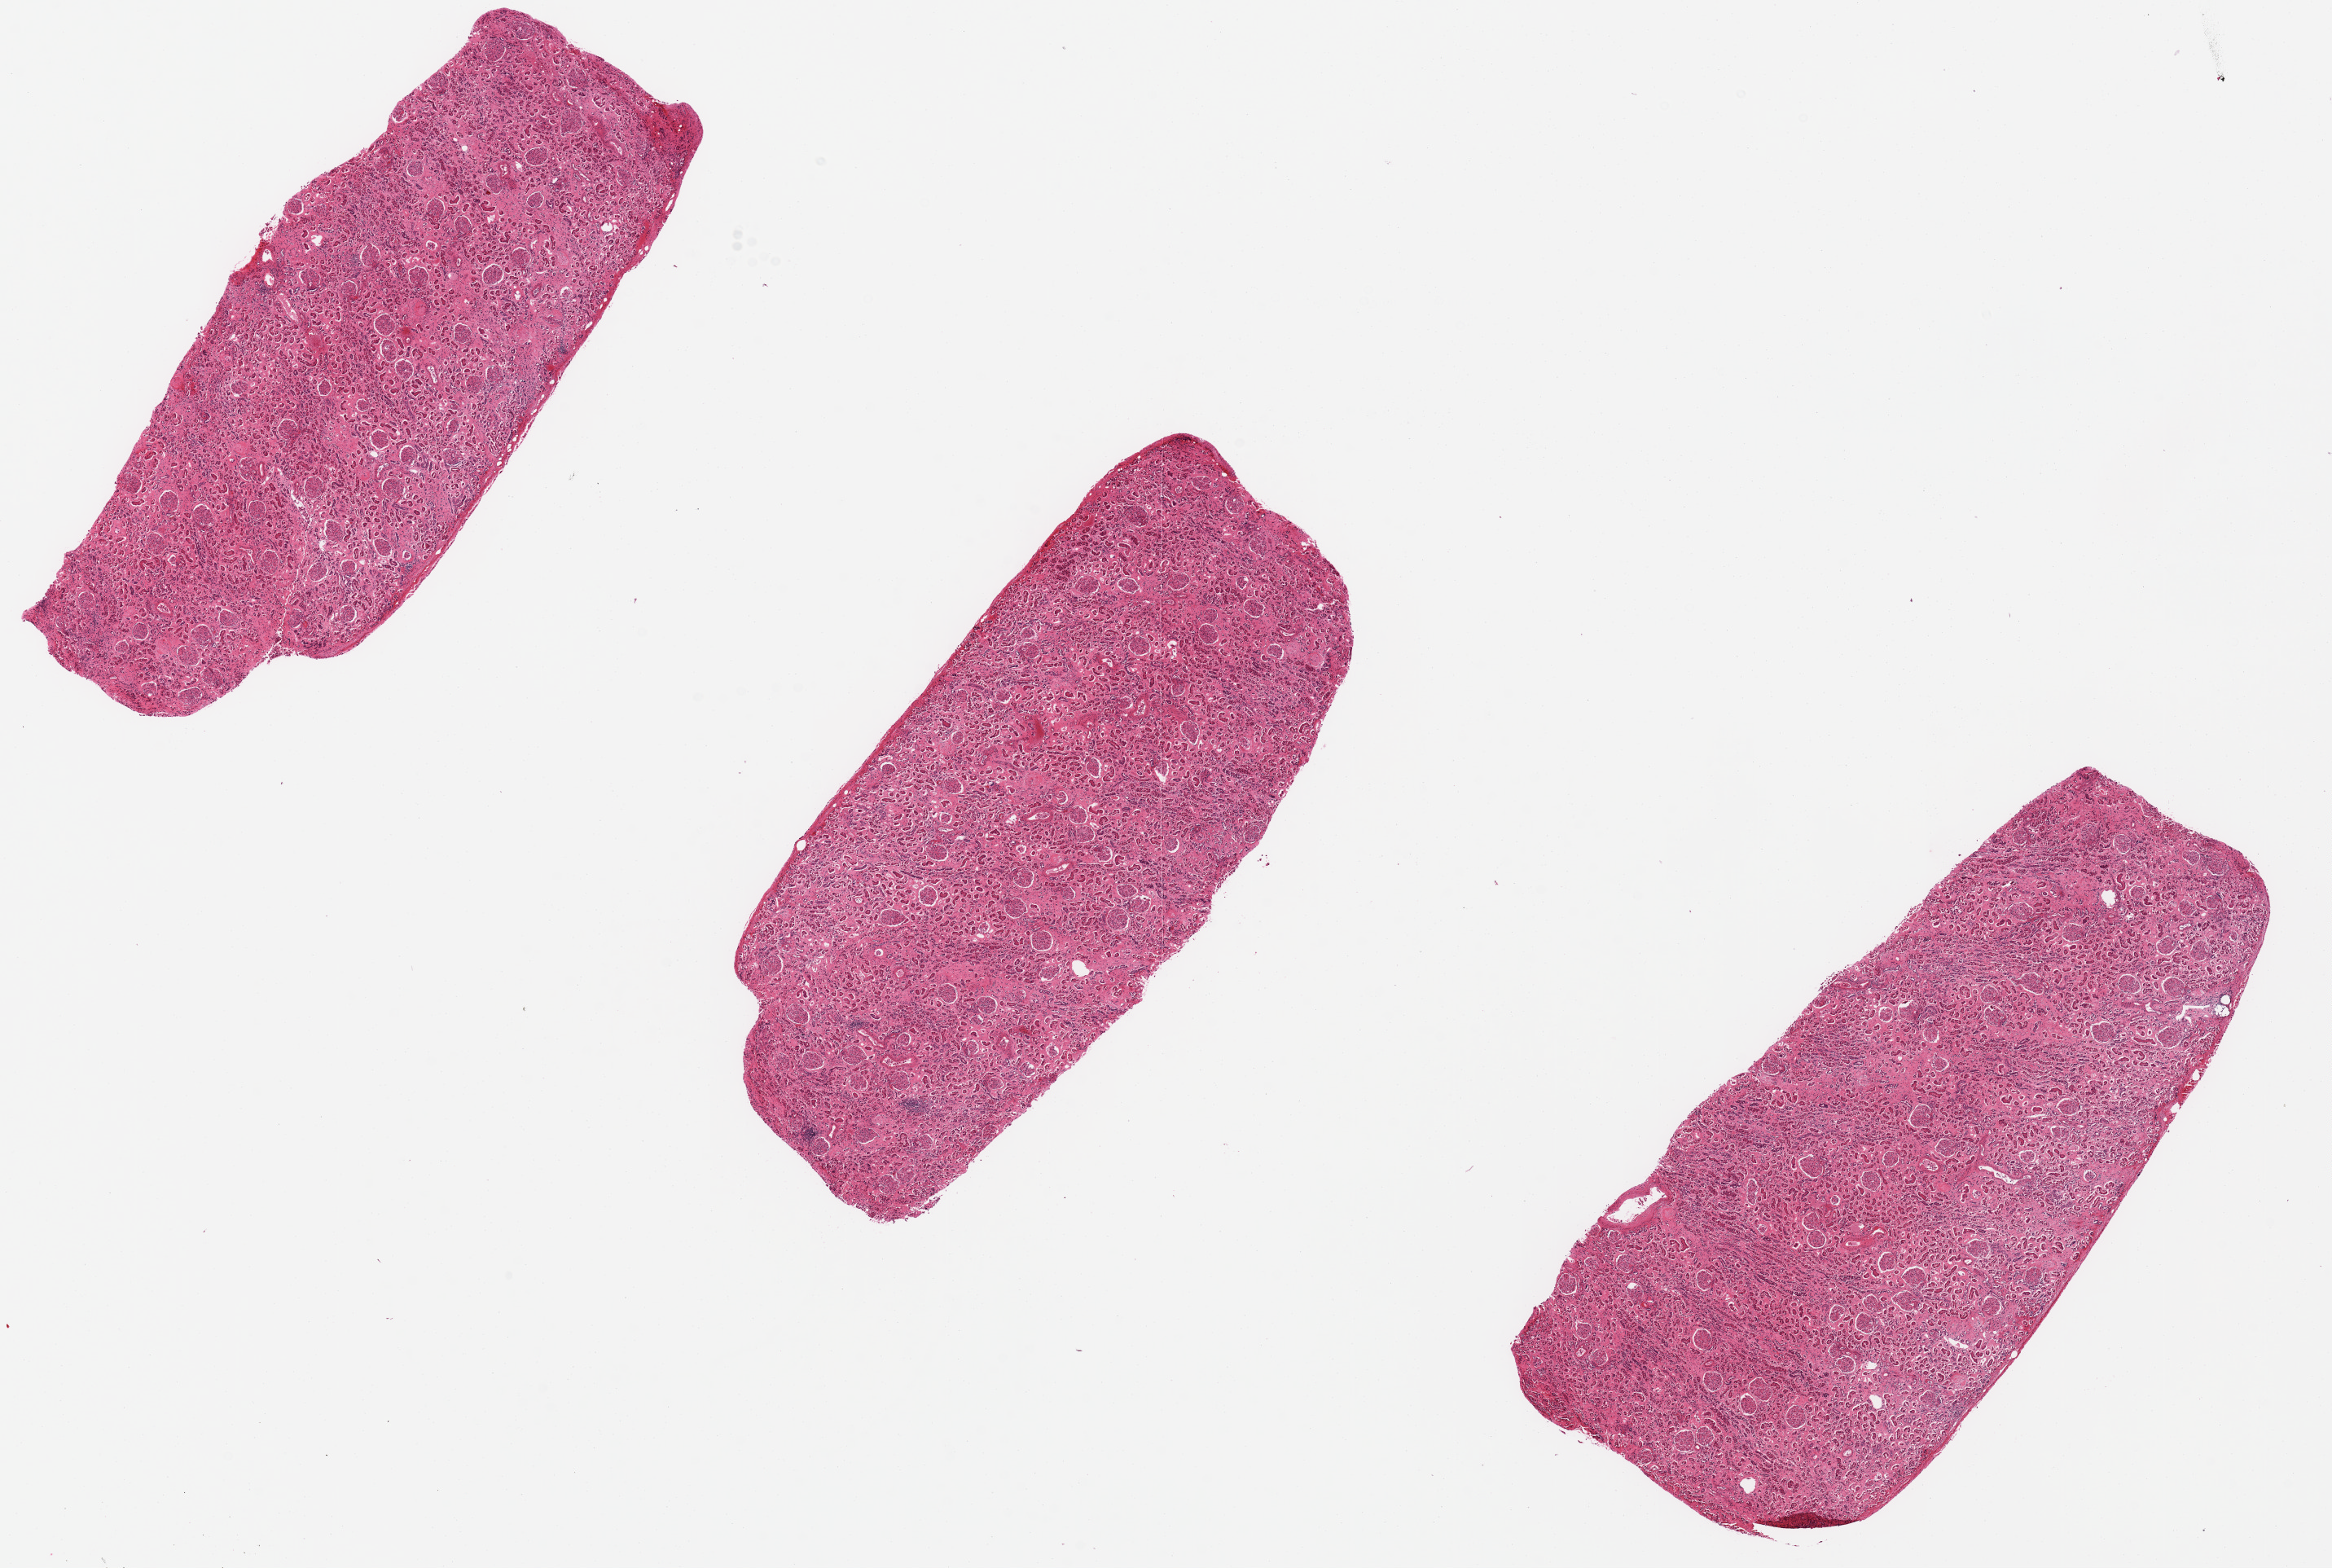
Digitized haematoxylin and eosin-stained section — low-resolution overview of the scanned area, about 22.6 x 15.2 mm (acquisition: 20x scan), PAXgene-fixed paraffin-embedded (PFPE) section, sampled site (target tissue): renal cortex, tissue donor sample.
• reviewer comment on this tissue sample: moderate arteriolar and glomerular sclerosis